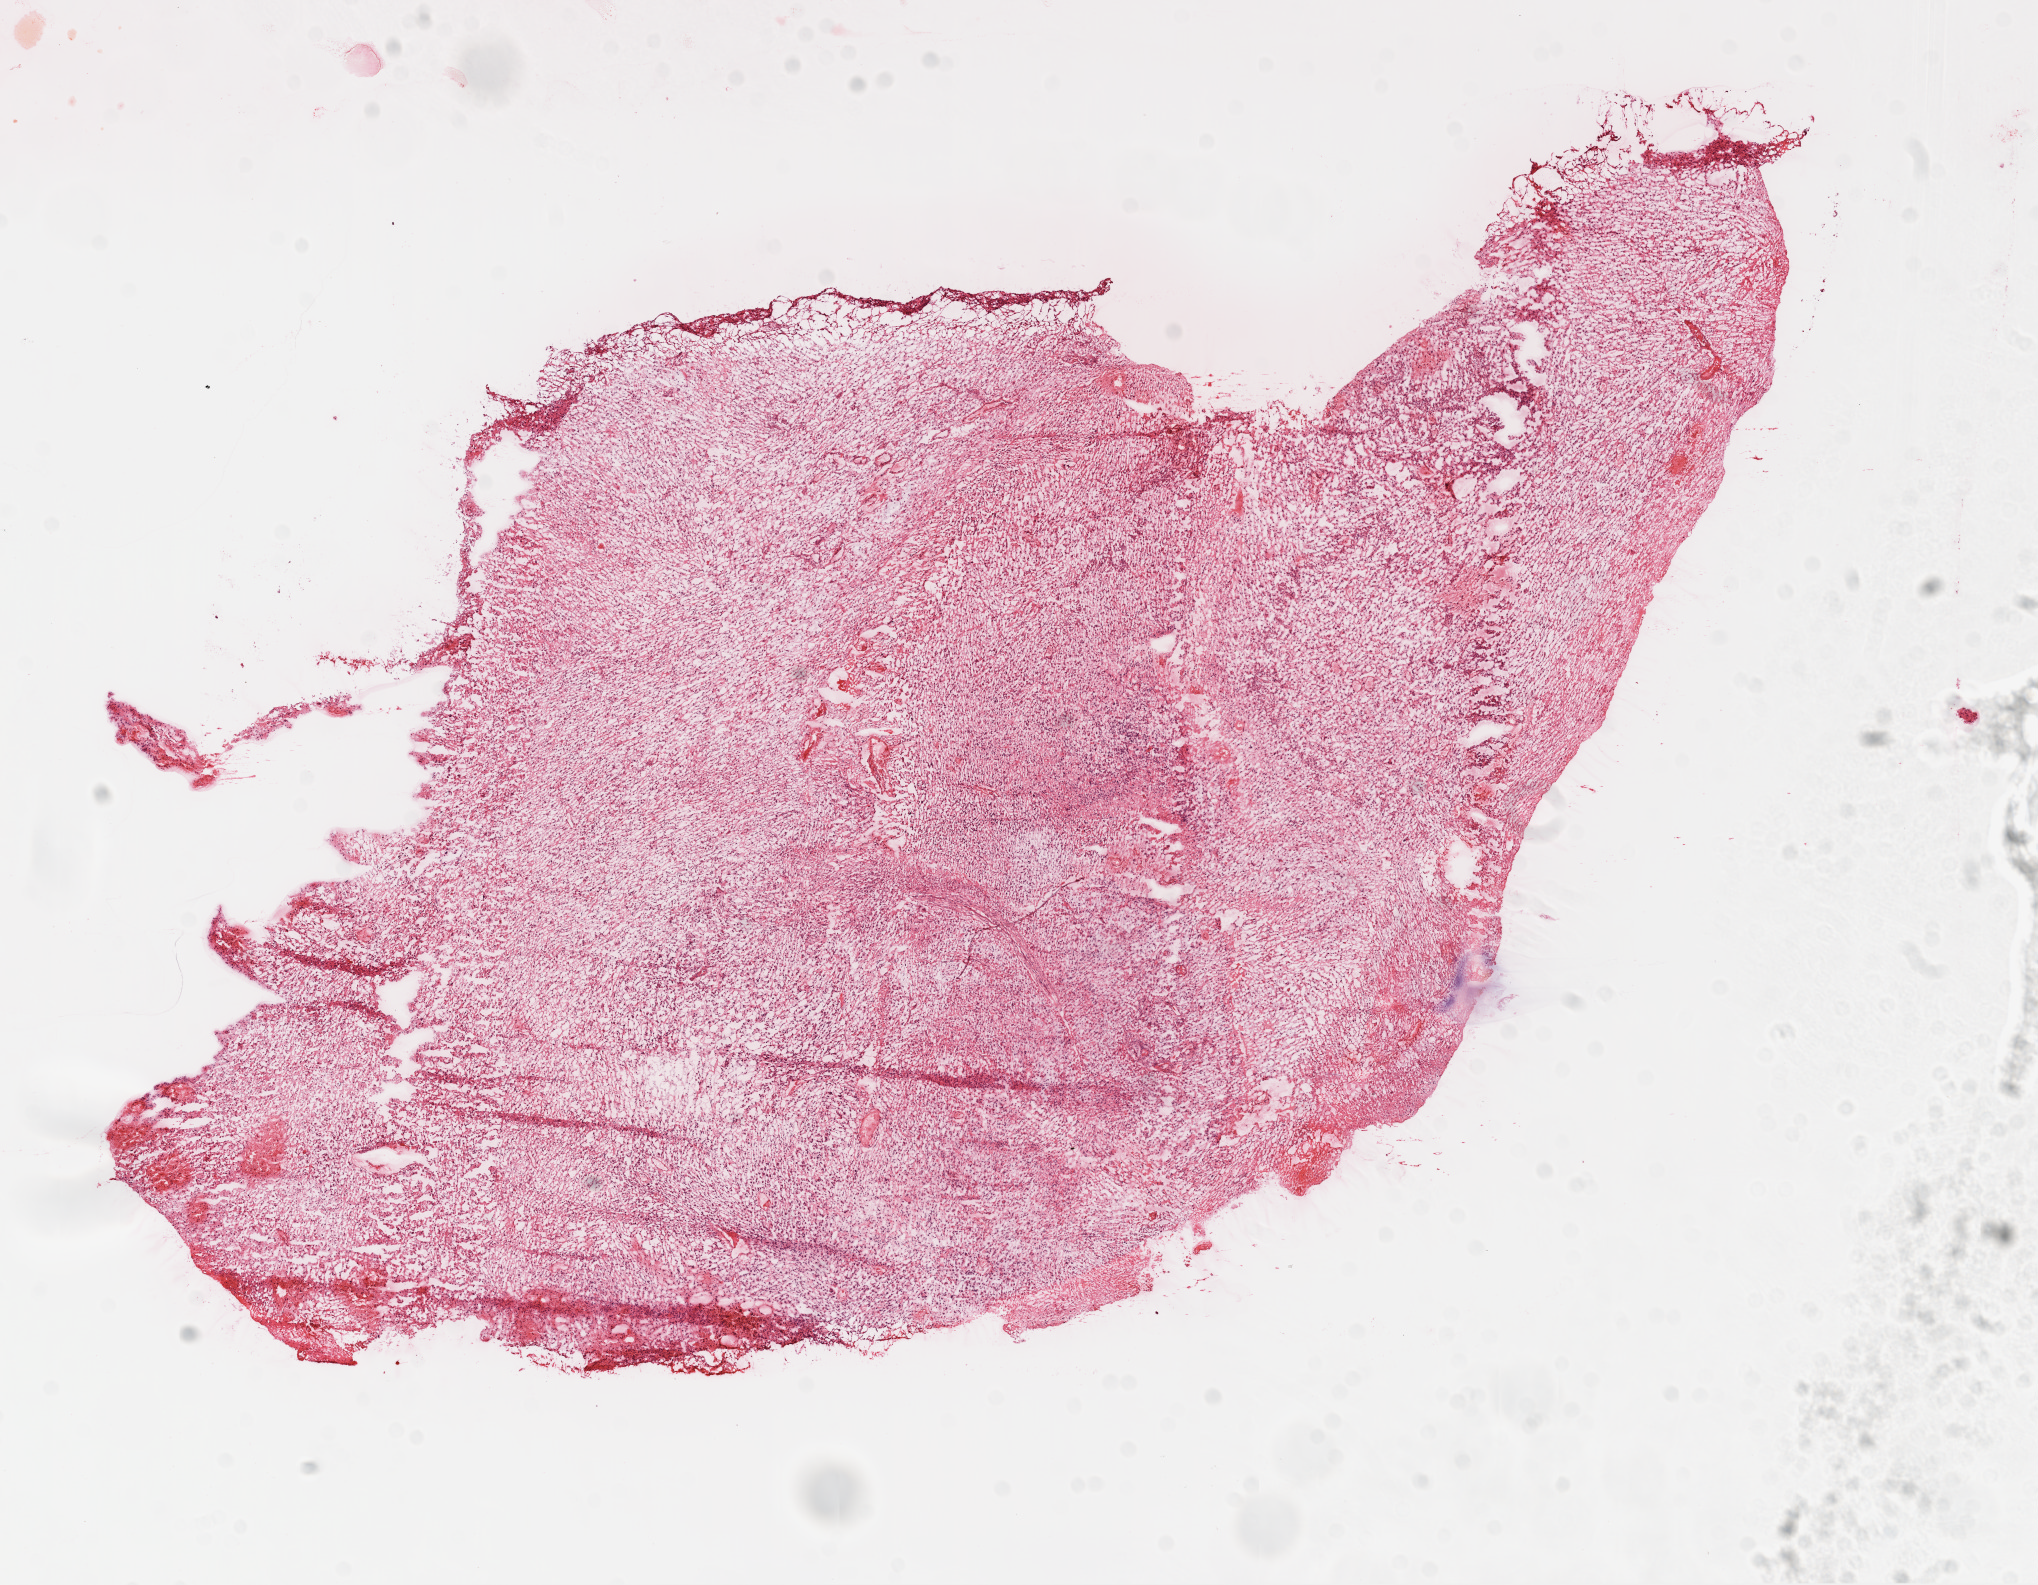
Digitized Hematoxylin and eosin (H&E) stained tissue section (whole slide), low-resolution overview of the scanned area, about 16.4 x 12.8 mm. Frozen section. Primary tumour sample from the brain. Patient: female, age at initial diagnosis 68 years. Pathologist review of this section (percent, as recorded): tumour cells 85%, tumour nuclei 90%, stromal cells 10%, necrosis 5%.
Pathologic diagnosis: Glioblastoma.